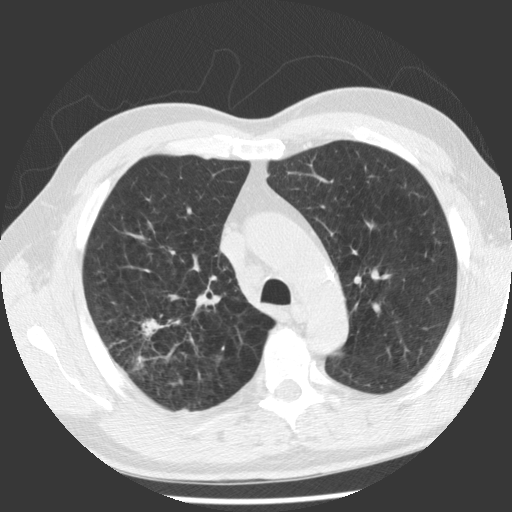
Low-dose screening chest CT, one axial slice. Slice 80 of 112 in the series (ordered by position). 140 kVp. Lung window (W 1500 / L -600 HU). 512 × 512 image matrix, field of view 344 × 344 mm.
Annotated regions visible in this slice (expert manual segmentation):
- lesion 1 (tumor, upper lobe of right lung): box from (x=142, y=319) to (x=160, y=338) px